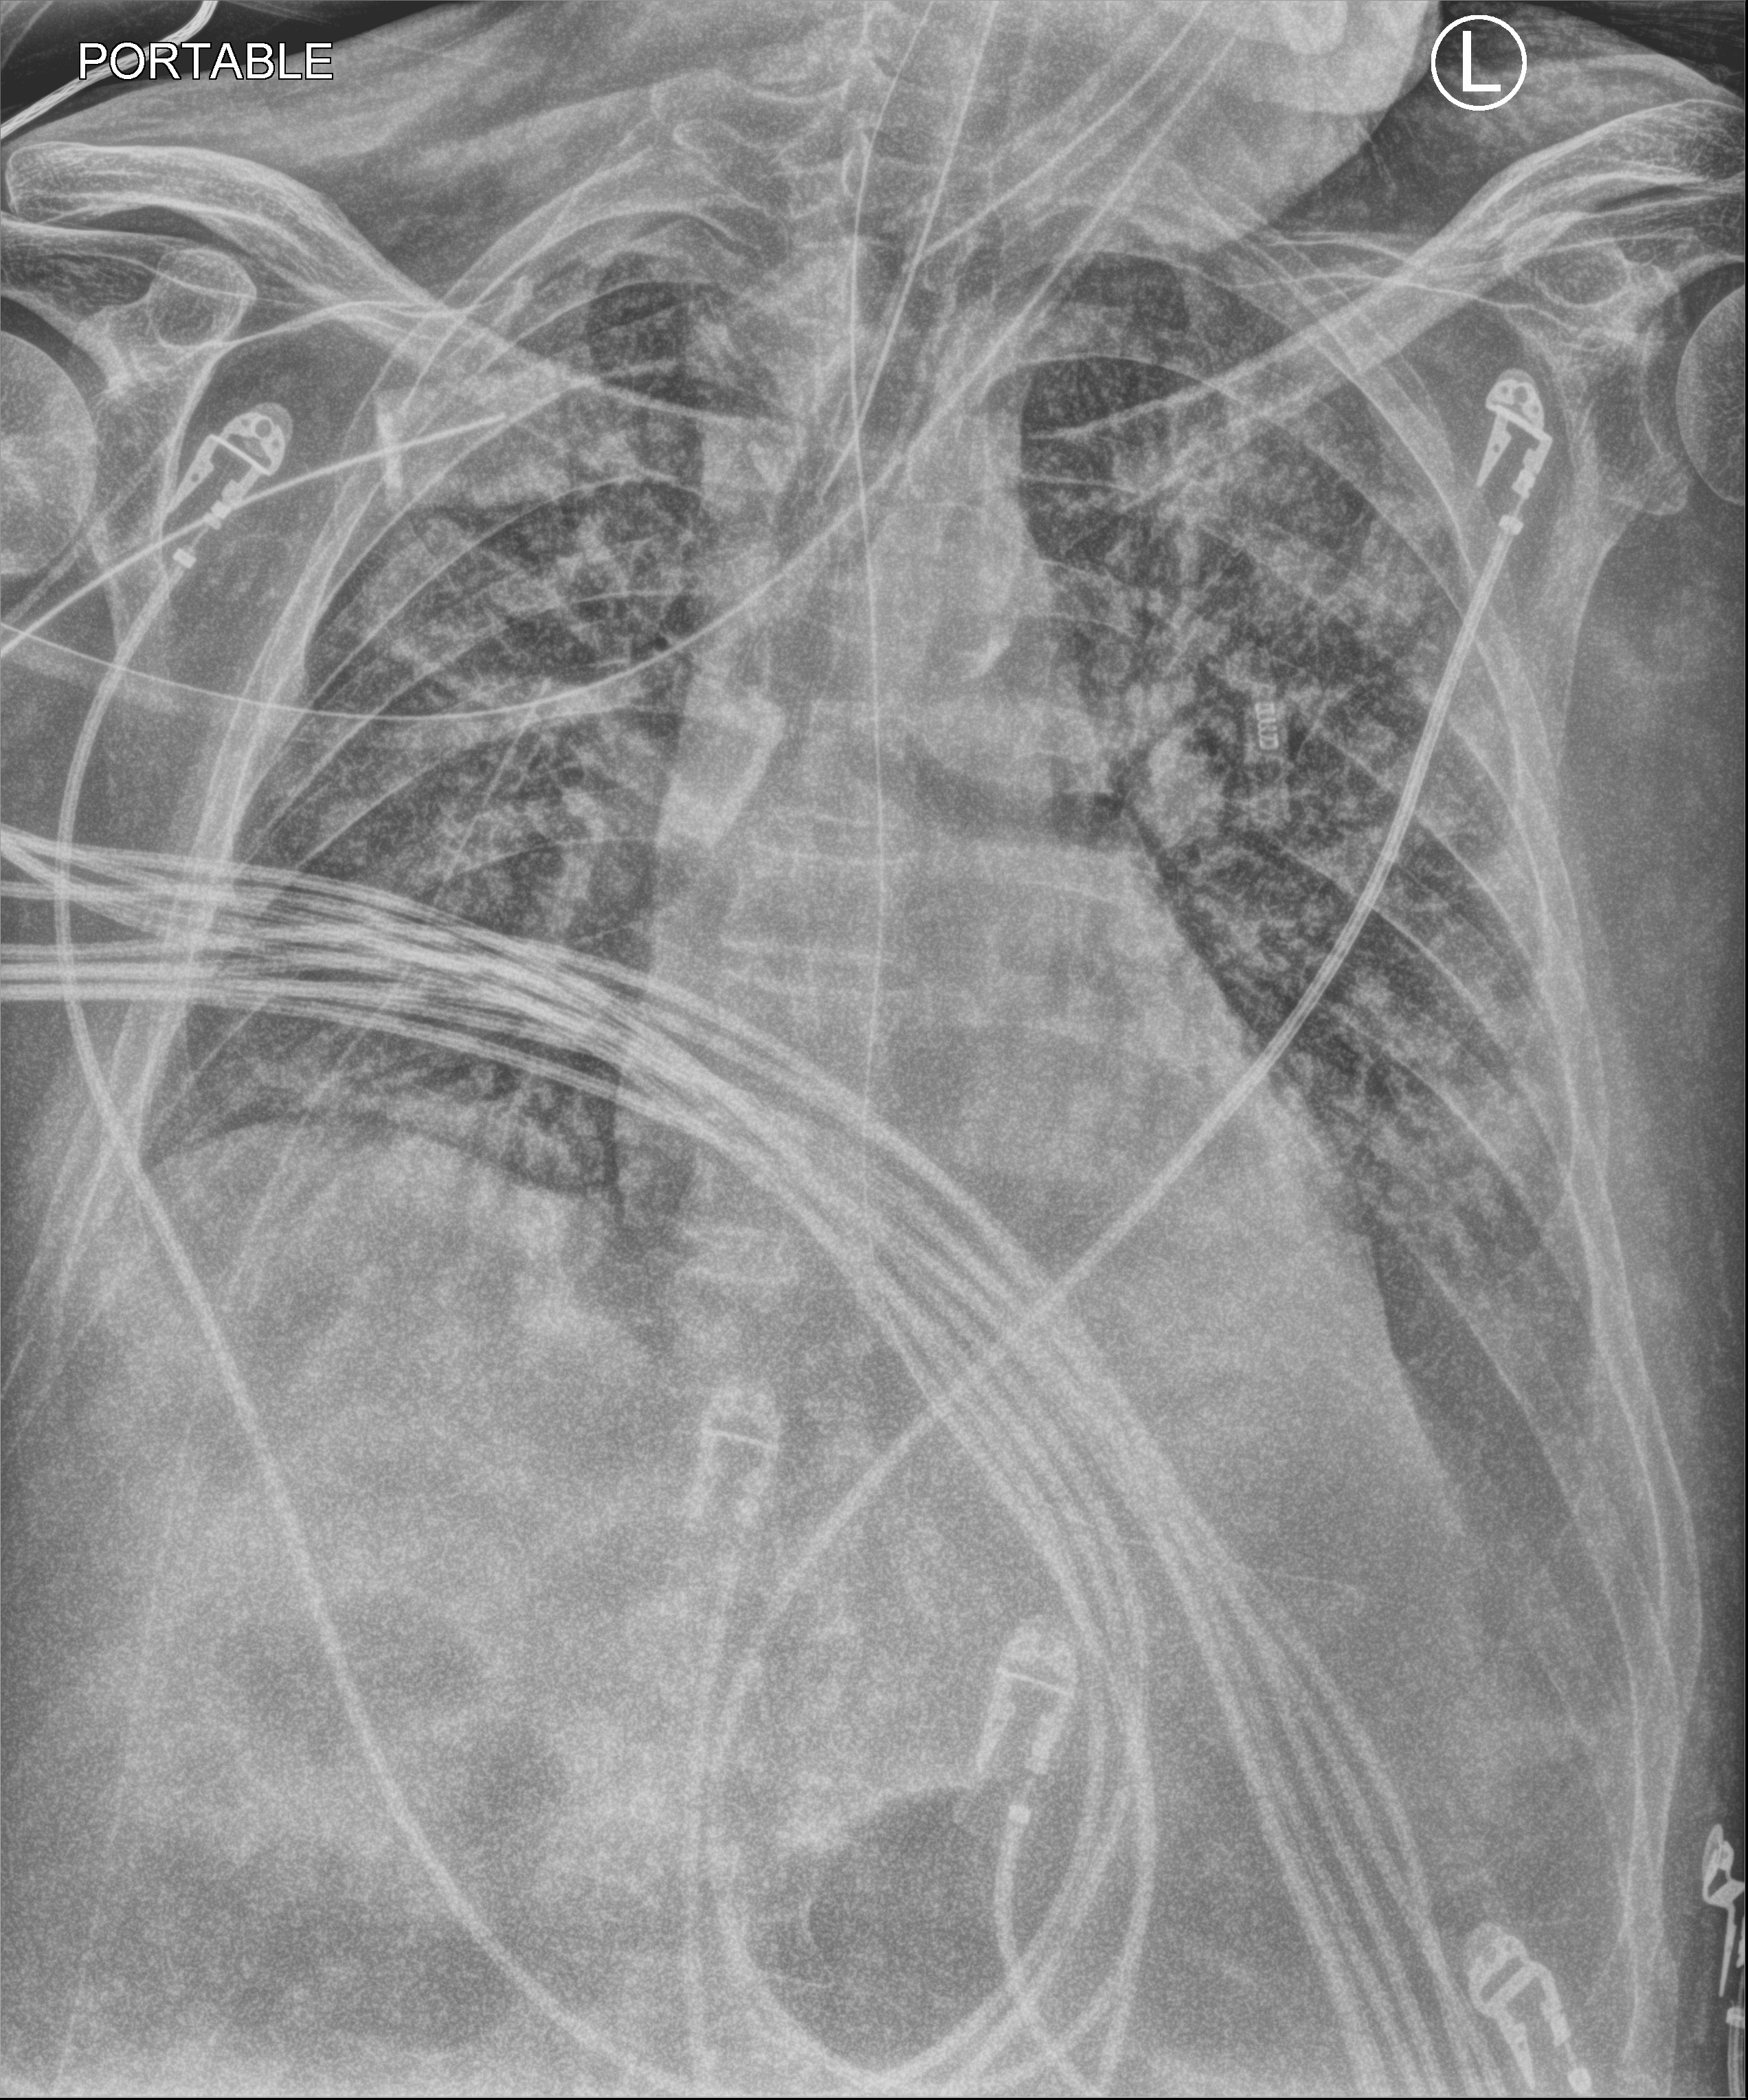
Chest X-ray (portable), anteroposterior (AP) projection. Patient hospitalised with COVID-19; male, aged 60–74 years.
Admission-level facts for this patient (not findings on this image; timing relative to this image not recorded):
- mechanically ventilated during this hospital stay: yes
- COPD (admission record): no
- diabetes (admission record): no